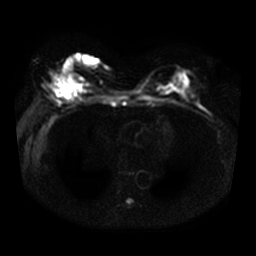
Breast MRI, one axial slice. Slice 18 of 36 in the series (ordered by position). Diffusion-weighted series; image 2 of 4 stored at this slice position (different b-values; order by instance number). 3 T. 5 mm slice thickness. 256 × 256 image matrix, field of view 330 × 330 mm. Female patient.
Outlined on this slice (expert manual segmentation):
- tumour on diffusion-weighted imaging: box from (x=53, y=78) to (x=75, y=98) px